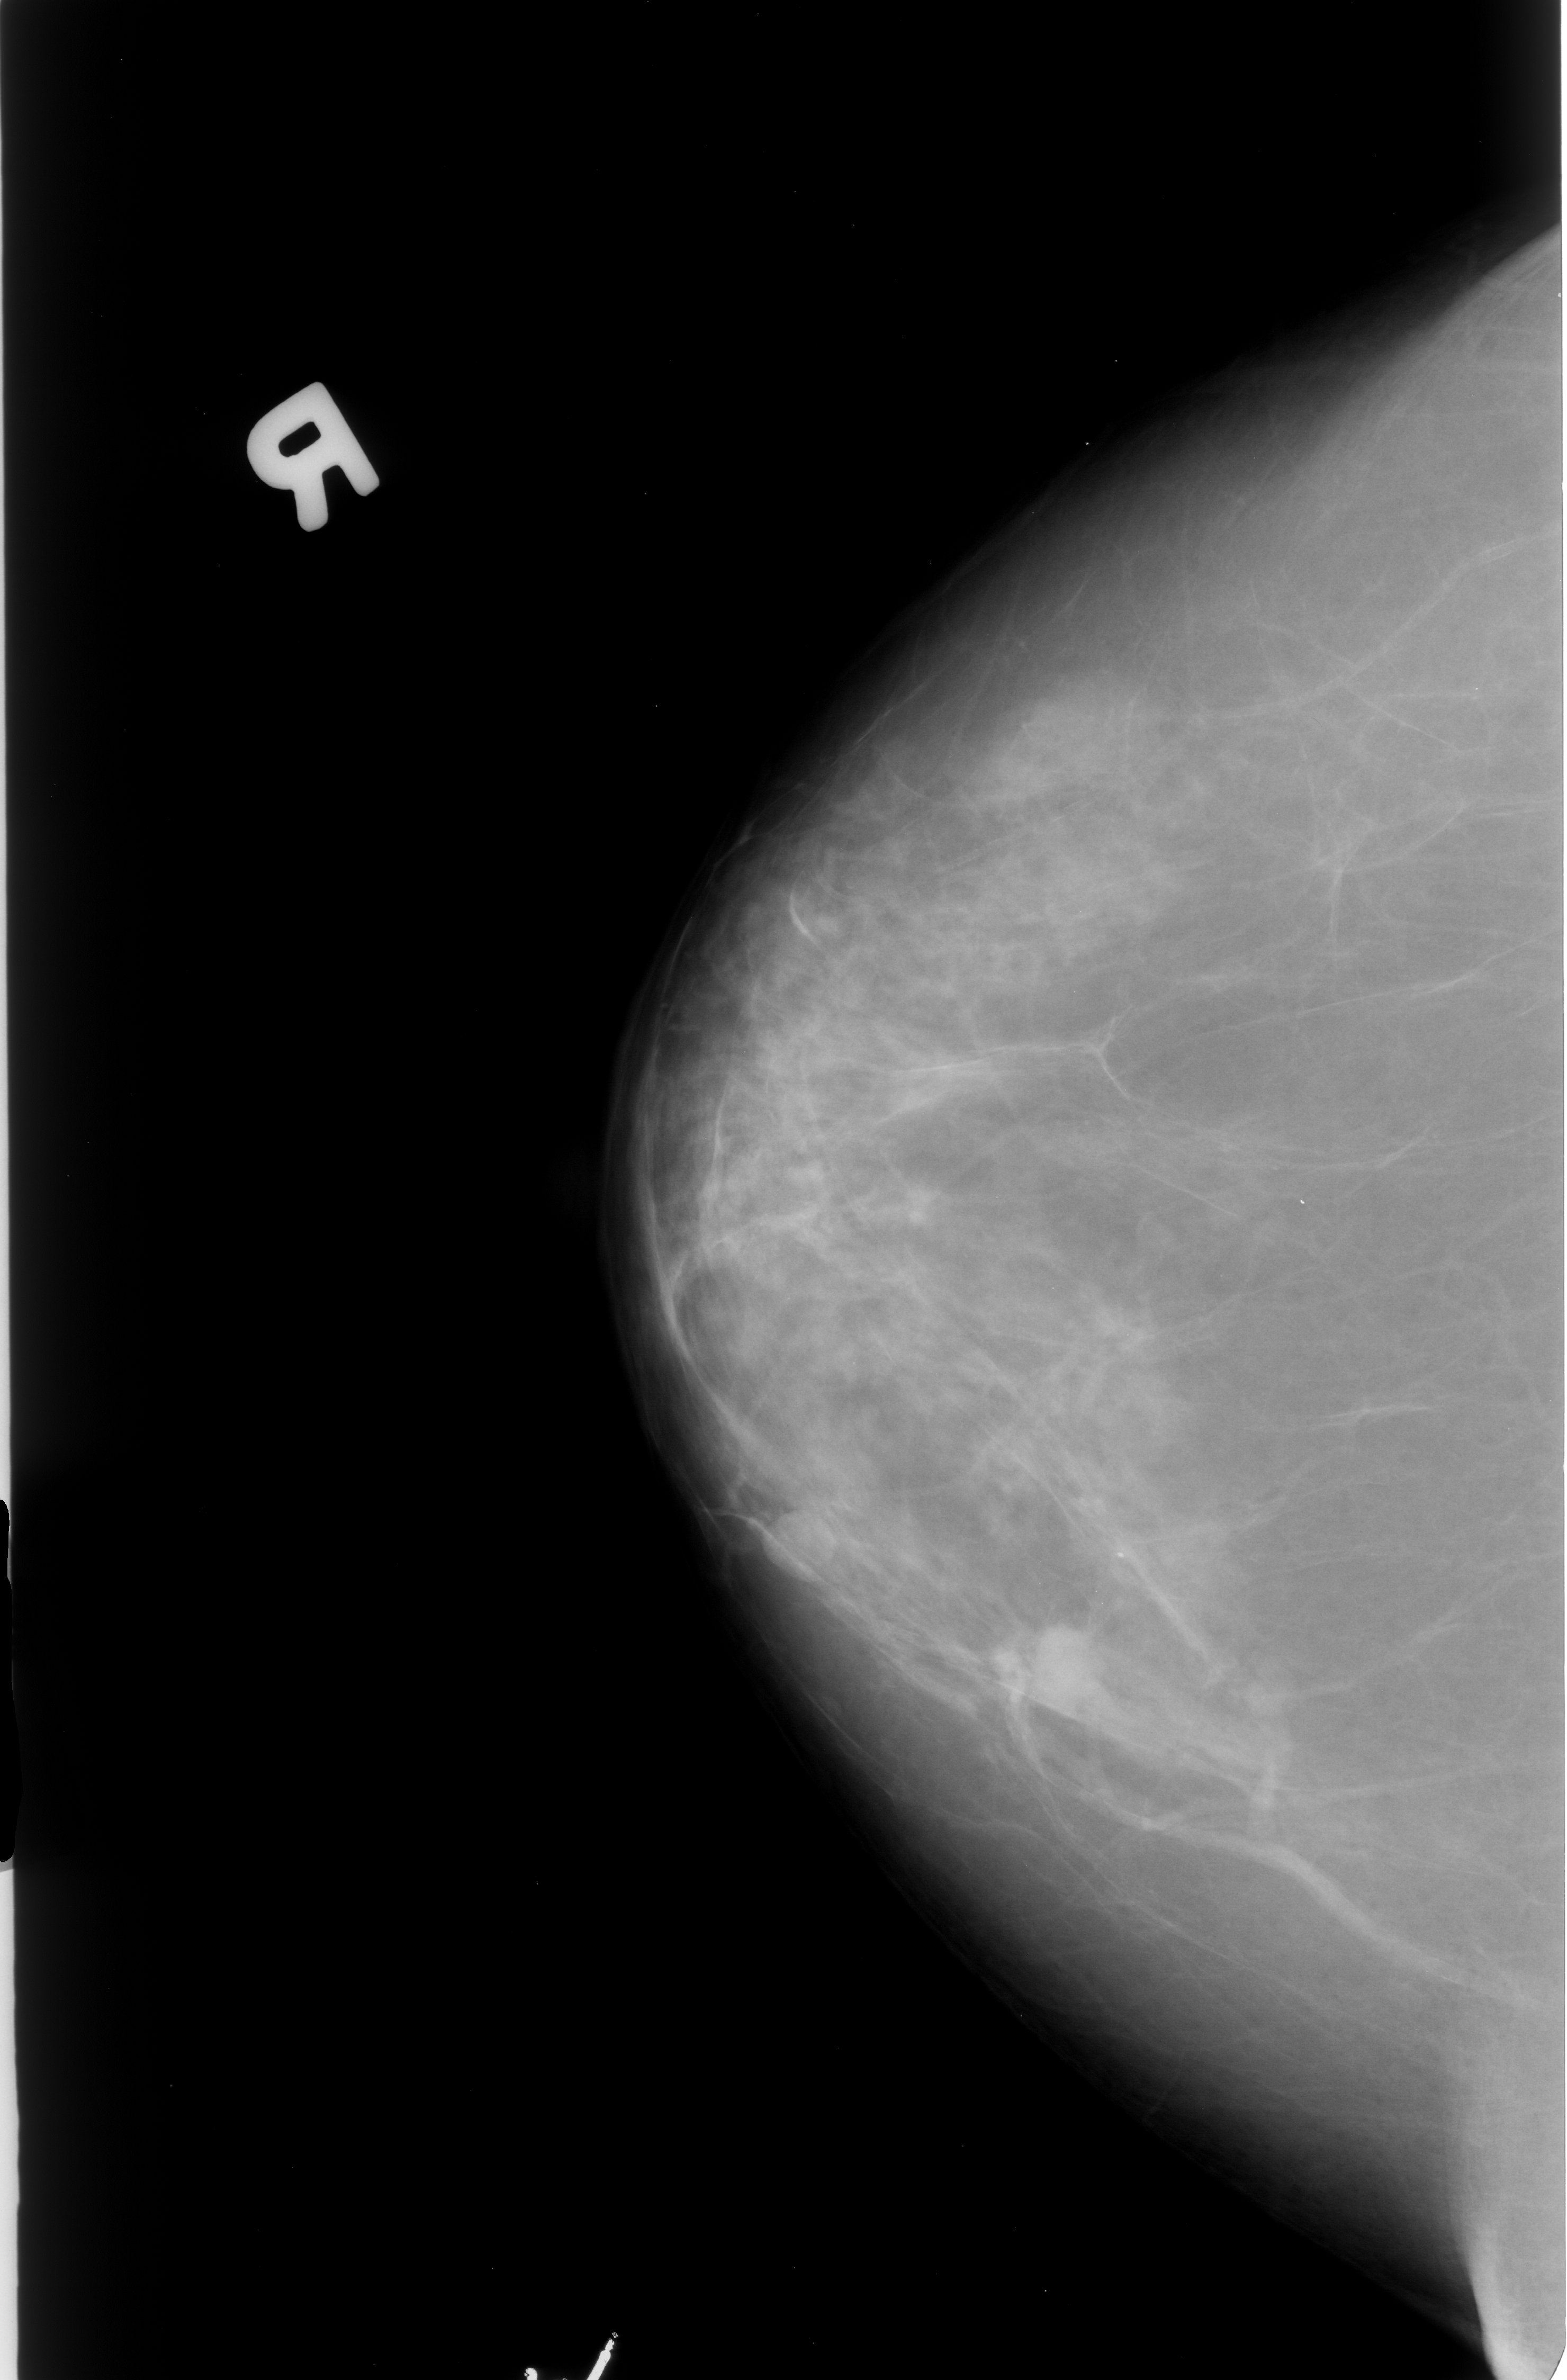
Digitized screen-film mammogram, right breast, craniocaudal (CC) view, breast composition: scattered fibroglandular densities (BI-RADS density category 2 of 4).
Mass, shape irregular / architectural distortion, margins microlobulated / ill defined / spiculated; BI-RADS assessment category 4; subtlety rating 4 on a 1 (subtle) to 5 (obvious) scale; pathology result (as recorded, not read from the image): malignant.